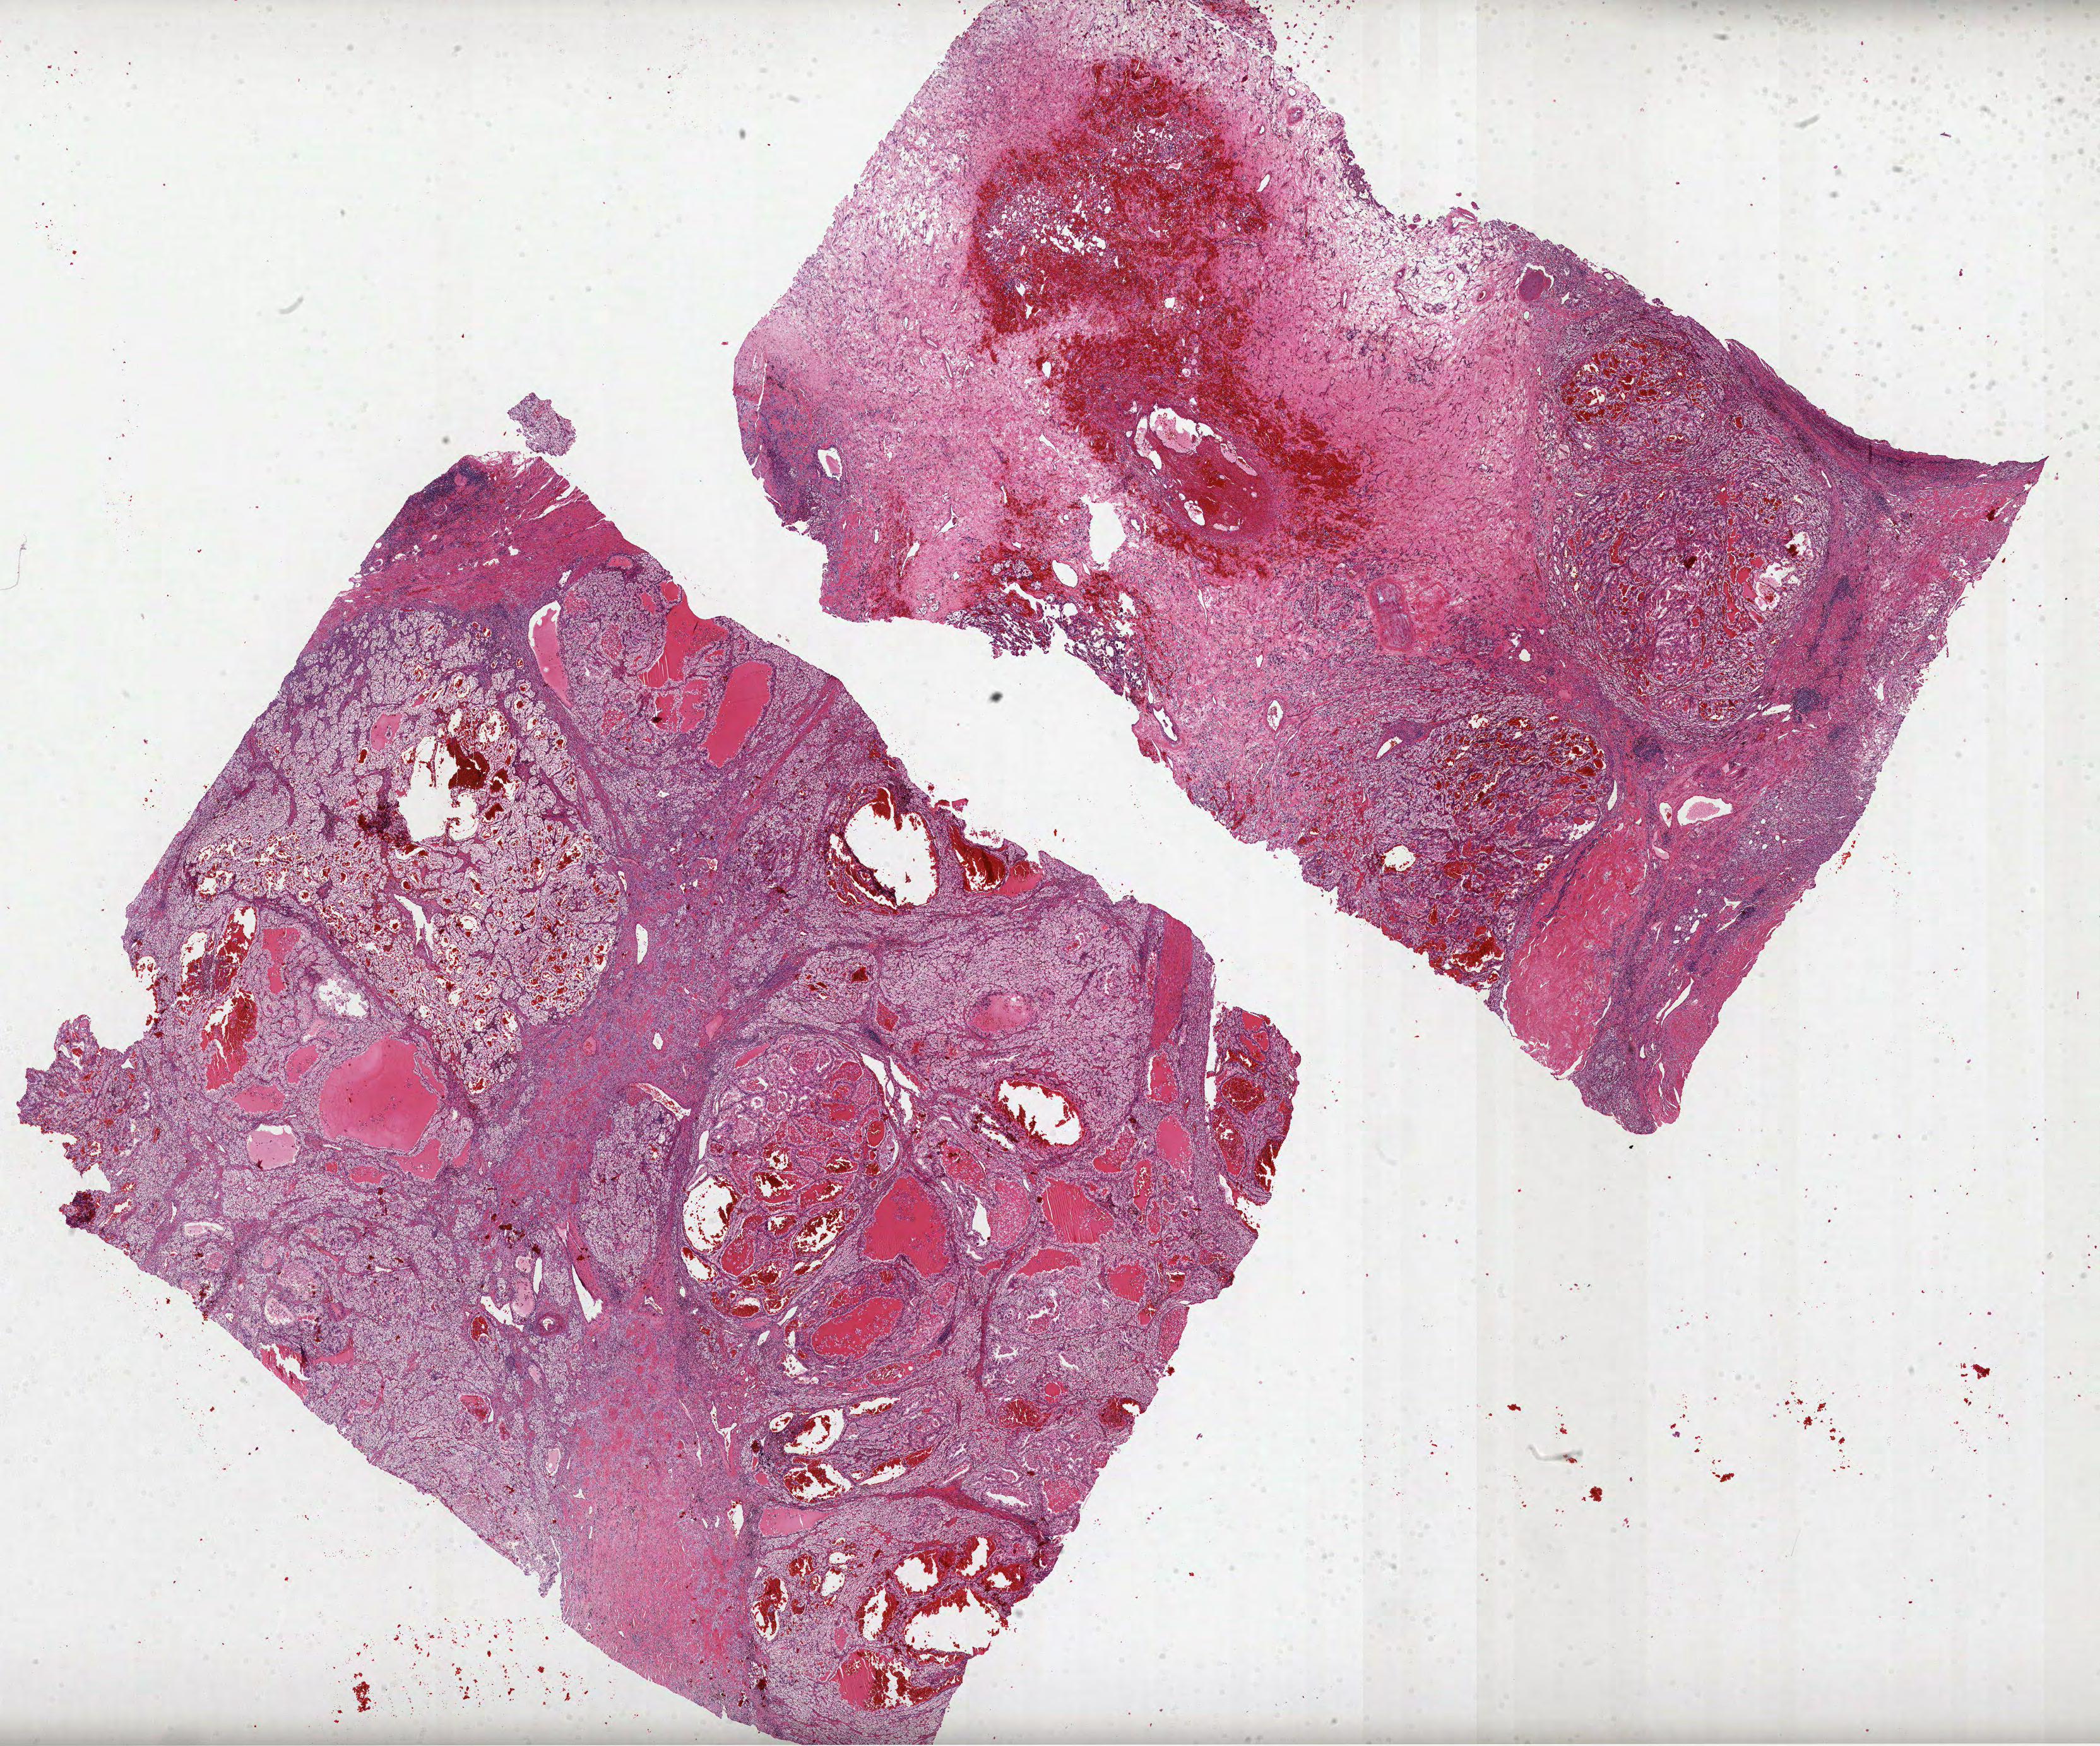
Digitized H&E tissue section (whole slide), low-resolution overview of the scanned area, about 26.8 x 22.3 mm (acquisition: 40x scan); FFPE section; primary tumour sample from the kidney. Male patient; age at initial diagnosis 53 years. Histologic grade: G3 (poorly differentiated).
Histologic diagnosis: Clear cell adenocarcinoma, NOS. AJCC pathologic stage: I. Laterality: right.